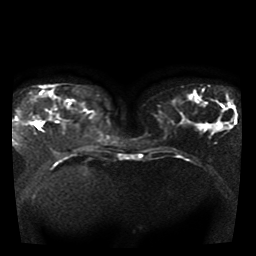
Breast MRI, one axial slice; slice 15 of 41 in the series (ordered by position); diffusion-weighted series; image 2 of 4 stored at this slice position (different b-values; order by instance number); 1.5 T; 5 mm slice thickness; 256 × 256 image matrix. Female patient.
Annotated regions visible in this slice (outlined manually by an expert reader):
- tumour on diffusion-weighted imaging: bounding box (x1, y1, x2, y2) in pixels: (22, 114, 40, 124)